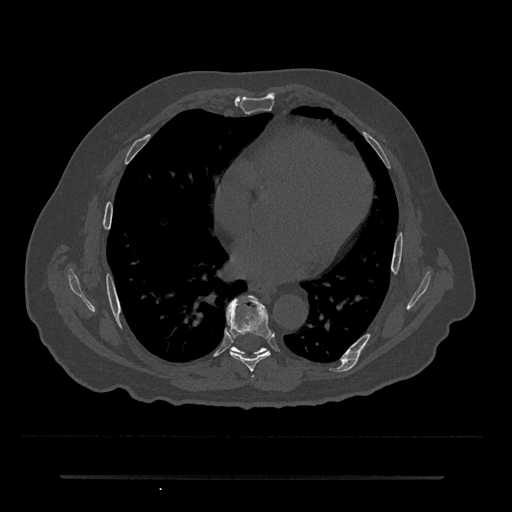
CT including the spine, one axial slice; position 369 of 797 along the scan axis; 120 kVp; bone window (W 1800 / L 400 HU); 512 × 512 image matrix. Male patient, age 69 years. Case-level facts recorded for this patient, not image findings: primary cancer: prostate.
Outlined on this slice (semi-automatically segmented with operator editing):
- T7 vertebra: box from (x=226, y=295) to (x=272, y=372) px
- T8 vertebra: (x=230, y=347)–(x=266, y=355)